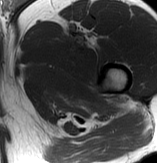
MRI of an extremity soft-tissue mass, one axial slice. Position 69 of 70 along the scan axis. MR volume resampled by the dataset authors to the PET/CT grid (not the native acquisition matrix). 3.27 mm slice thickness. 157 × 163 image matrix, field of view 153 × 159 mm. Male patient. From the clinical record (not read from this slice): histological type: extraskeletal osteosarcoma; grade: high; site of the primary tumour: left adductur.
Annotated regions visible in this slice (expert contour drawn on MRI and transferred to this co-registered scan by the dataset authors):
- gross tumour volume (mass): bounding box [x1, y1, x2, y2] px = [38, 24, 128, 121]